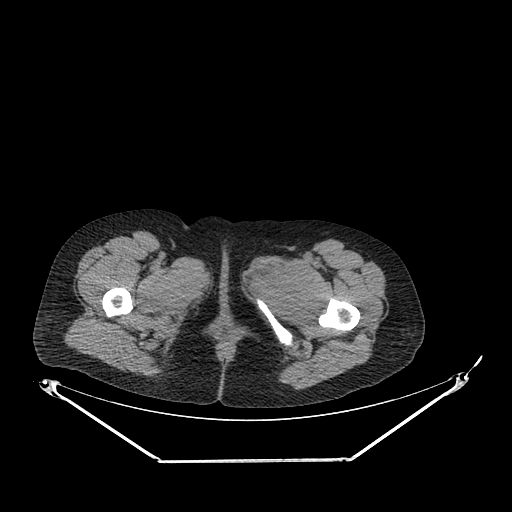
CT of an extremity soft-tissue mass (from a PET/CT study), one axial slice; position 255 of 267 along the scan axis; reconstruction kernel SOFT; 120 kVp; soft-tissue window (W 400 / L 40 HU); 3.75 mm slice thickness; 512 × 512 image matrix, field of view 500 × 500 mm. Female patient. From the clinical record (not read from this slice): histological type: pleiomorphic leiomyosarcoma; grade: intermediate; site of the primary tumour: left thigh.
Annotated regions visible in this slice (expert contour drawn on MRI and transferred to this co-registered scan by the dataset authors):
- gross tumour volume including surrounding oedema: bounding box <247,258,314,309> (left, top, right, bottom; pixels)
- gross tumour volume (mass): <265,262,314,307>